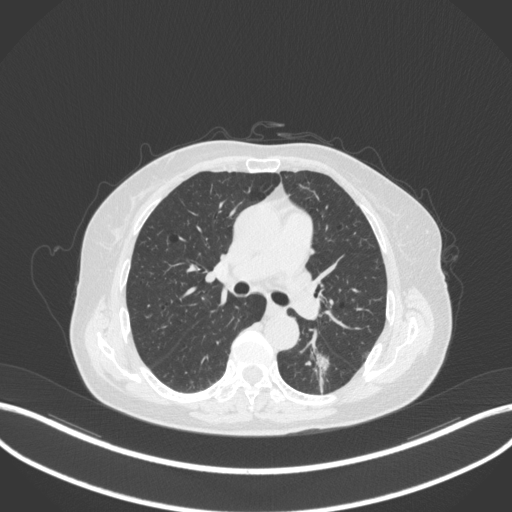
Chest CT, one axial slice; position 177 of 352 along the scan axis; lung window (W 1500 / L -600 HU); 512 × 512 image matrix, field of view 400 × 400 mm. Female patient, age 70 years. From the clinical record (not read from this slice): clinical TNM (as recorded): T1c N0 M0.
Annotated regions visible in this slice (rectangle marked by the reading radiologist):
- lung tumour (recorded histology: adenocarcinoma): box from (x=304, y=332) to (x=333, y=383) px